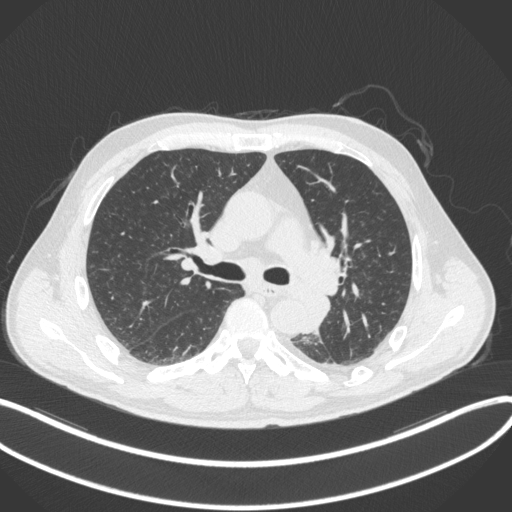
Chest CT, one axial slice. Slice 214 of 328 in the series (ordered by position). Lung window (W 1500 / L -600 HU). 512 × 512 image matrix. Male patient, age 59 years. Case-level facts recorded for this patient, not image findings: clinical TNM (as recorded): T2a N2 M0.
Structures marked on this image (bounding box drawn by a radiologist):
- lung tumour (recorded histology: squamous cell carcinoma): box from (x=303, y=287) to (x=333, y=334) px